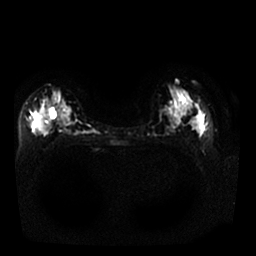
Breast MRI, one axial slice. Slice 13 of 25 in the series (ordered by position). Diffusion-weighted series; image 2 of 4 stored at this slice position (different b-values; order by instance number). 1.5 T. 4 mm slice thickness. 256 × 256 image matrix, field of view 340 × 340 mm. Female patient.
Structures marked on this image (expert manual segmentation):
- tumour on diffusion-weighted imaging: box from (x=34, y=114) to (x=46, y=133) px